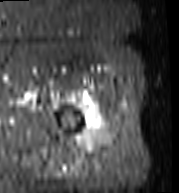
MRI of an extremity soft-tissue mass, one axial slice; STIR; MR volume resampled by the dataset authors to the PET/CT grid (not the native acquisition matrix); 3.27 mm slice thickness; 179 × 193 image matrix, field of view 175 × 188 mm. Female patient. From the clinical record (not read from this slice): histological type: undifferentiated – high grade; grade: high; site of the primary tumour: left thigh.
Structures marked on this image (expert contour drawn on MRI and transferred to this co-registered scan by the dataset authors):
- gross tumour volume including surrounding oedema: bounding box <79,108,106,150> (left, top, right, bottom; pixels)